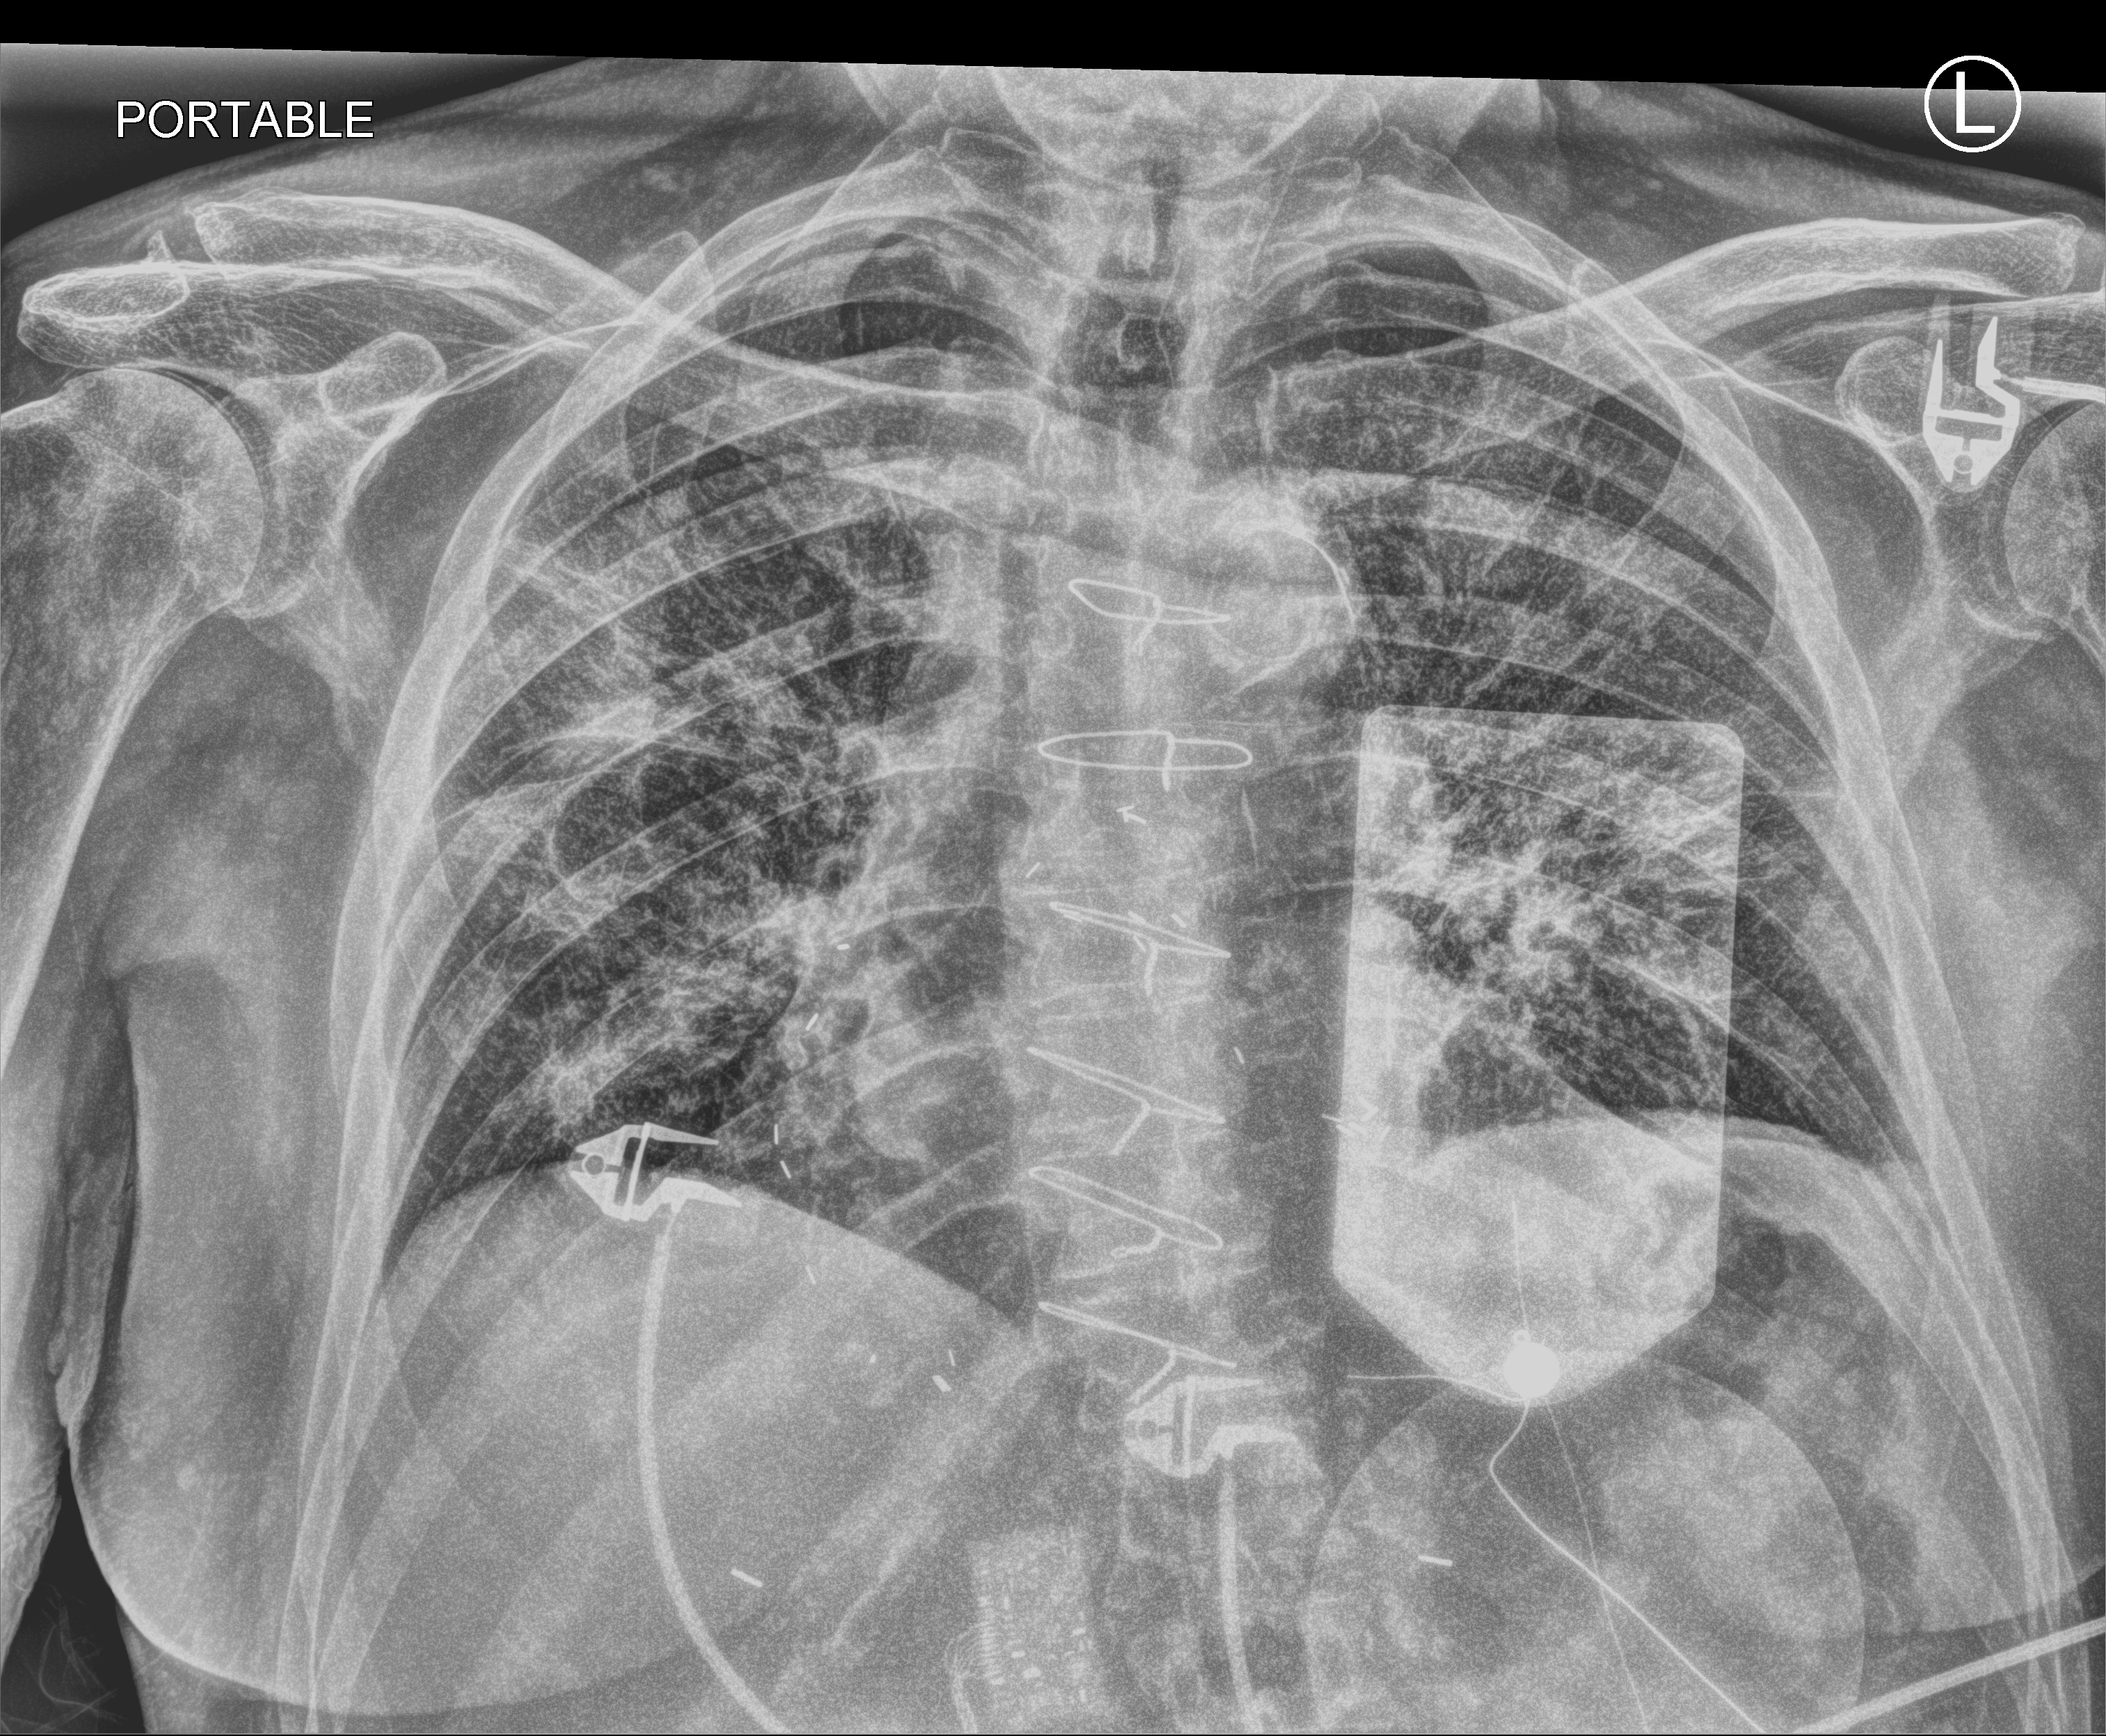
Bedside chest radiograph (computed radiography). Patient hospitalised with COVID-19; male, aged 75–90 years.
From the hospital-stay record, not from the radiograph (when in the stay this image was taken is not recorded):
- other chronic lung disease (admission record): no